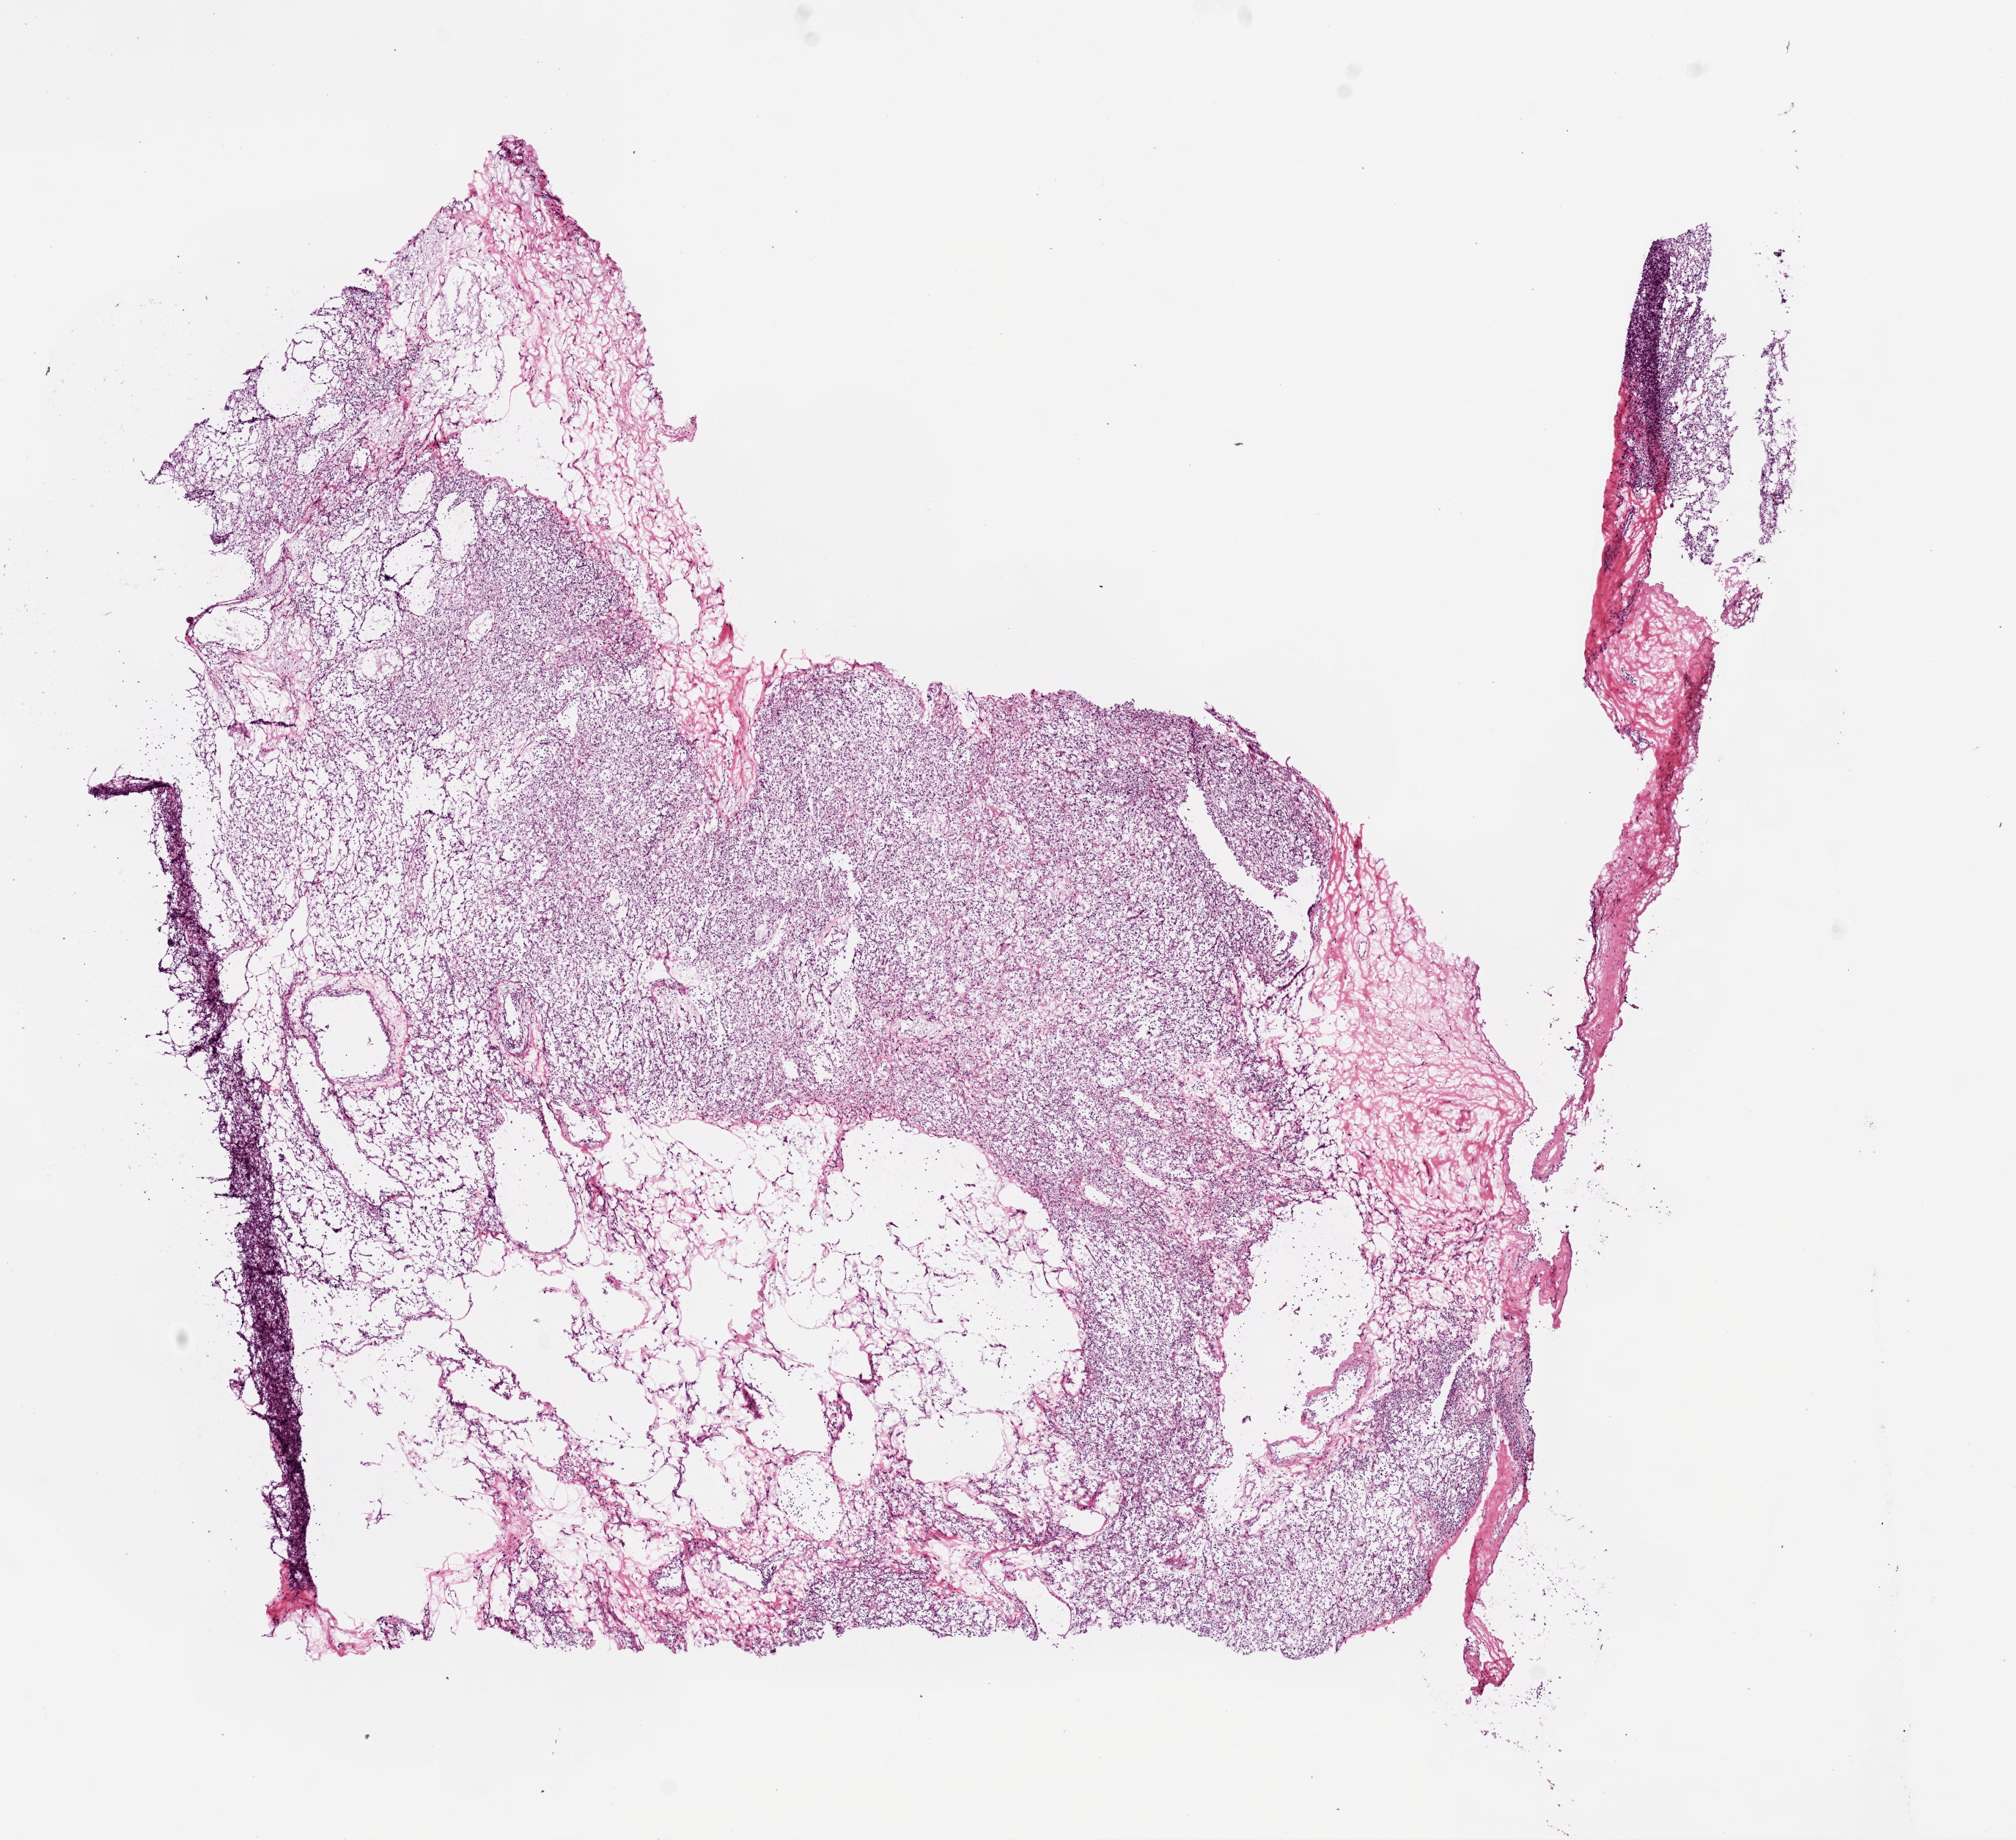
Digitized Hematoxylin and eosin (H&E) stained tissue section (whole slide) — a low-resolution overview of the entire scanned area, about 11.0 x 10.1 mm. Frozen section. Primary tumour sample from the kidney. Patient: female, age at initial diagnosis 53 years. Histologic grade: G1 (well differentiated). Pathologist review of this section (percent, as recorded): tumour cells 85%, tumour nuclei 80%, normal cells 0%, stromal cells 15%, necrosis 0%.
* diagnosis: Clear cell adenocarcinoma, NOS
* AJCC pathologic stage: I (6th edition)